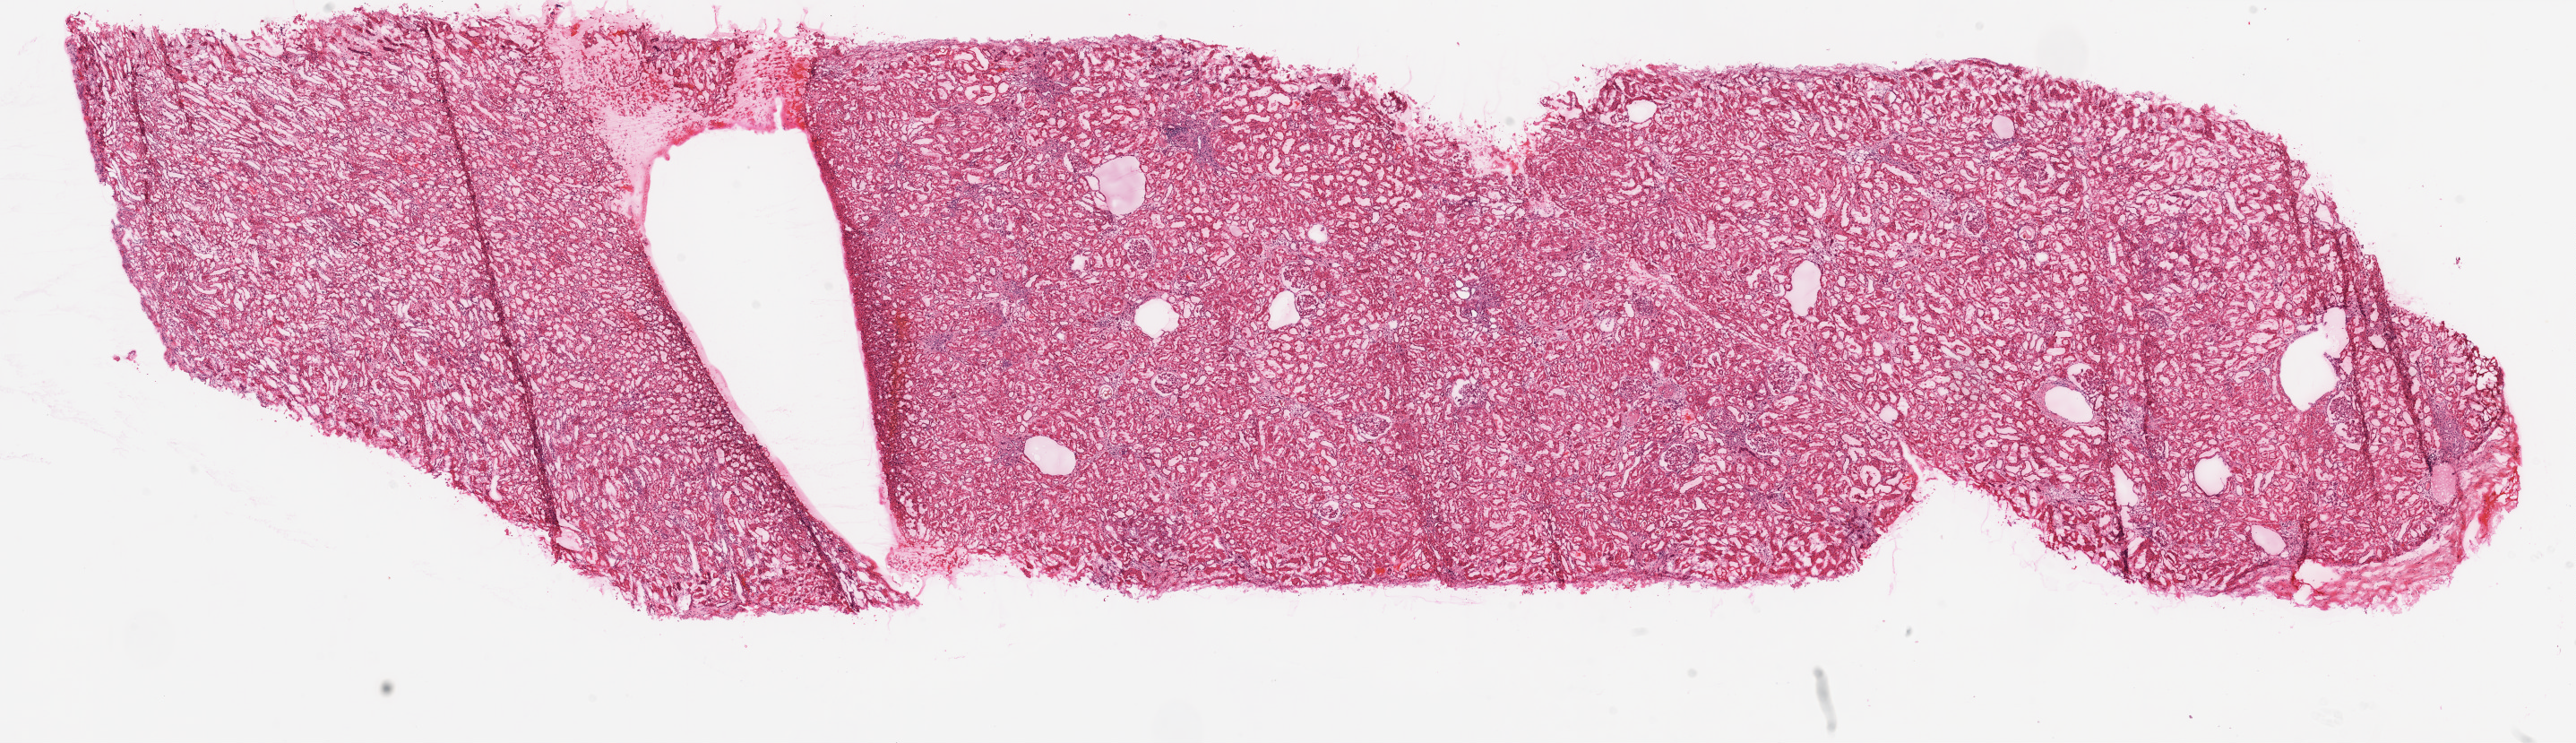
Digitized H&E tissue section (whole slide), low-resolution overview of the scanned area, about 23.1 x 6.7 mm, frozen section from the top of the tissue portion, sample: solid tissue normal (non-tumour tissue), kidney. Patient: male, age at initial diagnosis 50 years.
This section: solid tissue normal (non-tumour) sample from the same patient. Patient diagnosis: Clear cell adenocarcinoma, NOS.